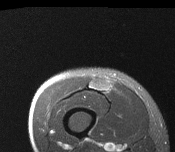
MRI of an extremity soft-tissue mass, one axial slice. Position 31 of 116 along the scan axis. T2-weighted fat-saturated. MR volume resampled by the dataset authors to the PET/CT grid (not the native acquisition matrix). 3.27 mm slice thickness. 175 × 152 image matrix, field of view 171 × 148 mm. Male patient. From the clinical record (not read from this slice): histological type: pleiomorphic leiomyosarcoma; grade: intermediate; site of the primary tumour: right thigh.
Structures marked on this image (expert contour drawn on MRI and transferred to this co-registered scan by the dataset authors):
- gross tumour volume including surrounding oedema: box from (x=90, y=79) to (x=109, y=93) px